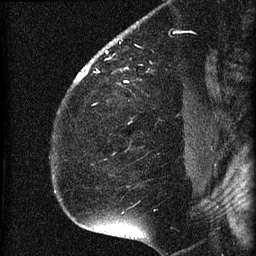
Breast MRI (dynamic contrast-enhanced), one sagittal slice. Slice 49 of 60 in the series (ordered by position). Dynamic contrast-enhanced series, image 2 of 4 at this slice position (ordered by acquisition). 1.5 T. TE 4.2 ms, TR 22.7 ms. 1.5 mm slice thickness. 256 × 256 image matrix. Female patient, age 35 years. Case-level facts recorded for this patient, not image findings: setting: breast cancer imaged before/during neoadjuvant chemotherapy; receptor status: HR-positive, HER2-negative.
Annotated regions visible in this slice (semi-automatic segmentation, software-assisted and operator-edited):
- analysis volume of interest (the breast-tissue region the enhancement analysis was run in; not a lesion): bounding box [x1, y1, x2, y2] px = [69, 27, 199, 112]
- tumour enhancement mask (voxels above the 90 % enhancement threshold inside the analysis volume of interest): [74, 51, 108, 82]